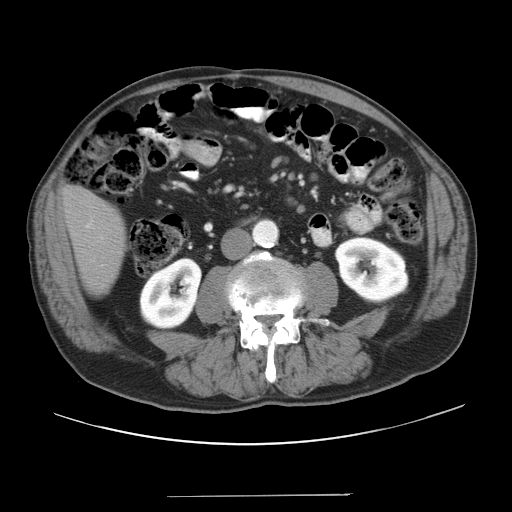
Contrast-enhanced abdominal CT, one axial slice. Slice 3 of 41 in the series (ordered by position). 120 kVp. Intravenous contrast given. Soft-tissue window (W 400 / L 40 HU). 5 mm slice thickness. 512 × 512 image matrix, field of view 420 × 420 mm. Male patient, age 75 years. Case-level facts recorded for this patient, not image findings: diagnosis: colorectal cancer liver metastases, imaged before liver resection; multiple liver metastases: no; largest metastasis: 5.2 cm; disease in both lobes: no.
Structures marked on this image (expert manual segmentation):
- liver: bounding box (x1, y1, x2, y2) in pixels: (64, 188, 125, 290)
- planned liver remnant (the part of the liver to remain after resection): (64, 188, 125, 291)
- portal vein (with intrahepatic branches): (86, 224, 90, 228)